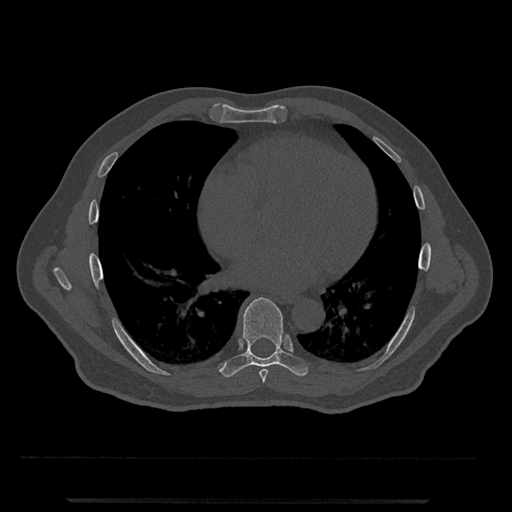
CT including the spine, one axial slice; slice 639 of 797 in the series (ordered by position); reconstruction kernel Br40s/3; bone window (W 1800 / L 400 HU); 512 × 512 image matrix, field of view 419 × 419 mm. Male patient, age 63 years. From the clinical record (not read from this slice): primary cancer: prostate.
Annotated regions visible in this slice (semi-automatic segmentation, software-assisted and operator-edited):
- T7 vertebra: bounding box [x1, y1, x2, y2] px = [259, 369, 268, 383]
- T8 vertebra: [220, 297, 308, 378]